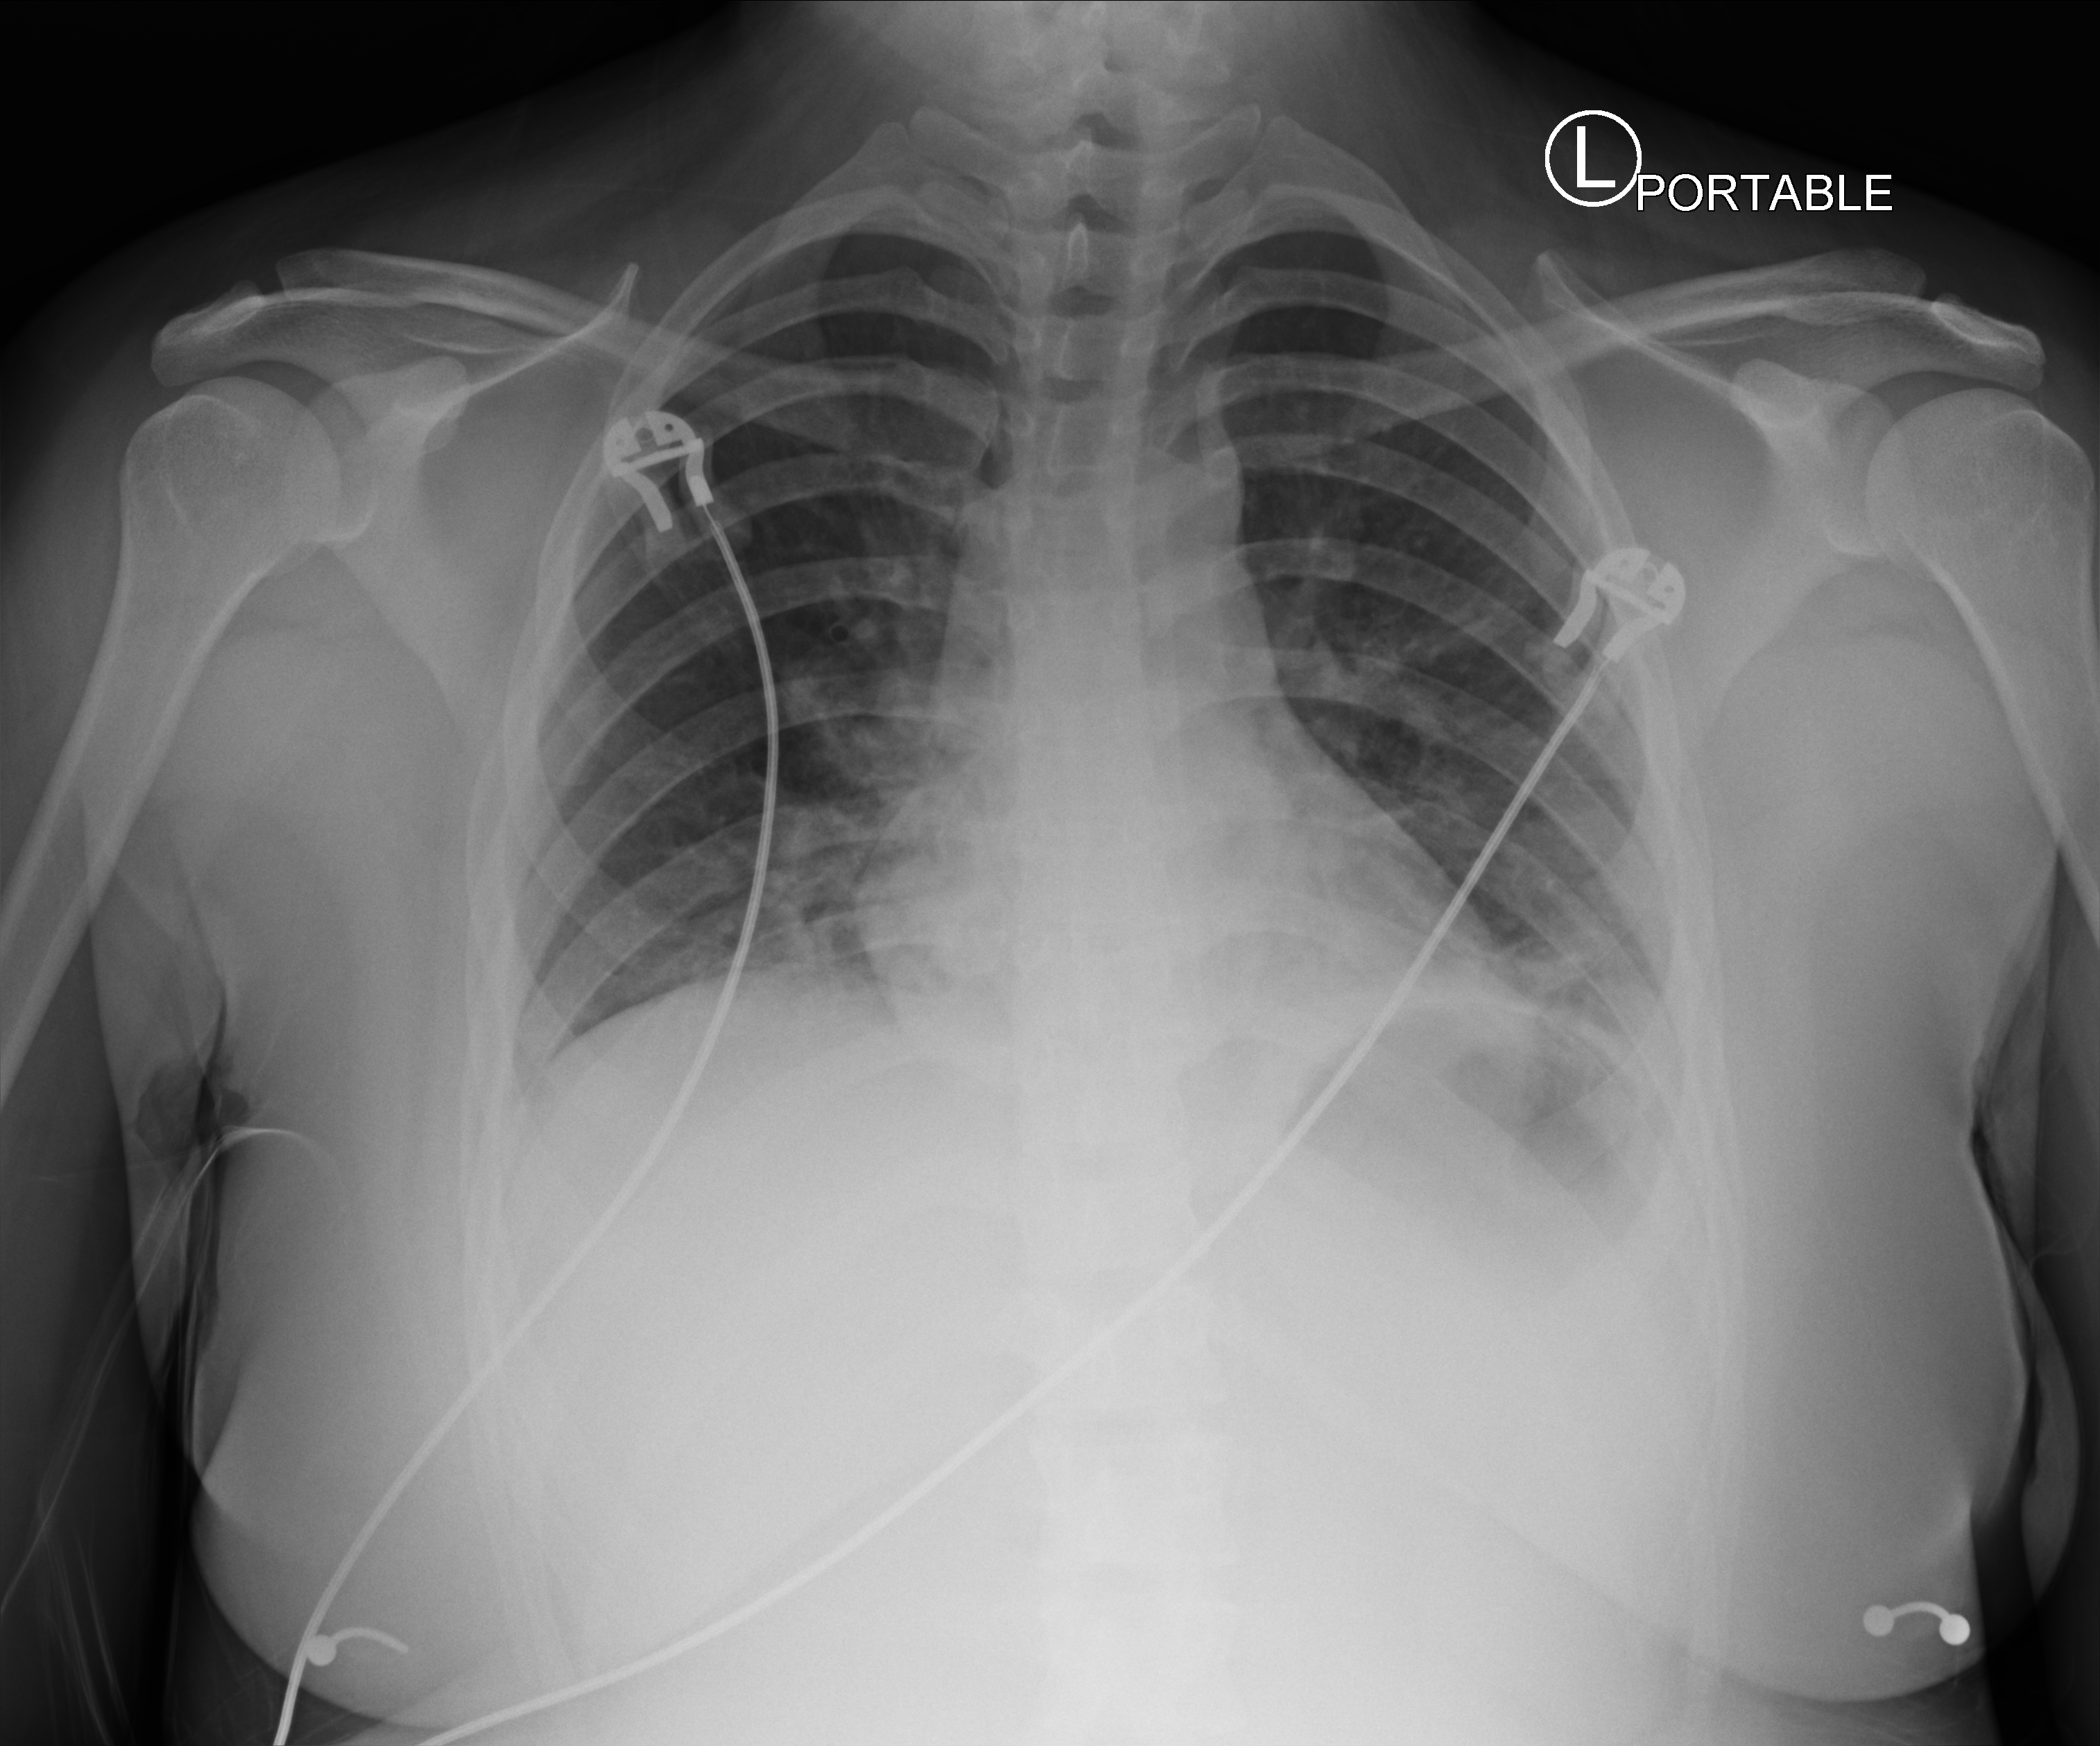
Portable chest radiograph; anteroposterior (AP) projection. Female patient hospitalised with COVID-19, age 18–59 years.
Hospital-stay facts (about this admission, not read from this image; timing relative to this image not recorded): length of hospital stay: 4 days; mechanically ventilated during this hospital stay: no; admitted to intensive care during this hospital stay: no.